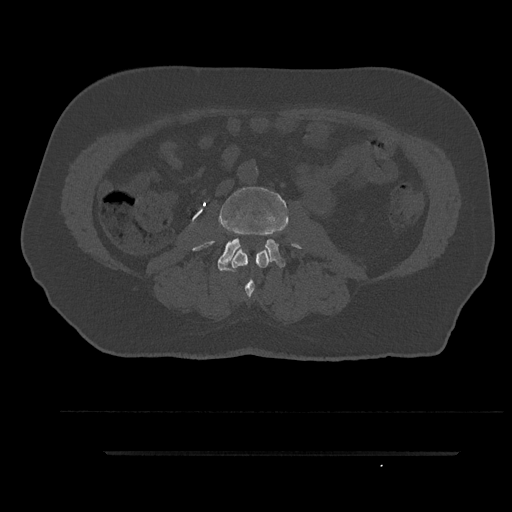
CT including the spine, one axial slice. Slice 68 of 797 in the series (ordered by position). Reconstruction kernel Br40s/3. 120 kVp. Bone window (W 1800 / L 400 HU). 0.5 mm slice thickness. 512 × 512 image matrix, field of view 432 × 432 mm. Male patient, age 63 years. Case-level facts recorded for this patient, not image findings: primary cancer: renal.
Annotated regions visible in this slice (semi-automatically segmented with operator editing):
- L2 vertebra: bounding box <232,250,269,299> (left, top, right, bottom; pixels)
- L3 vertebra: <193,185,300,271>